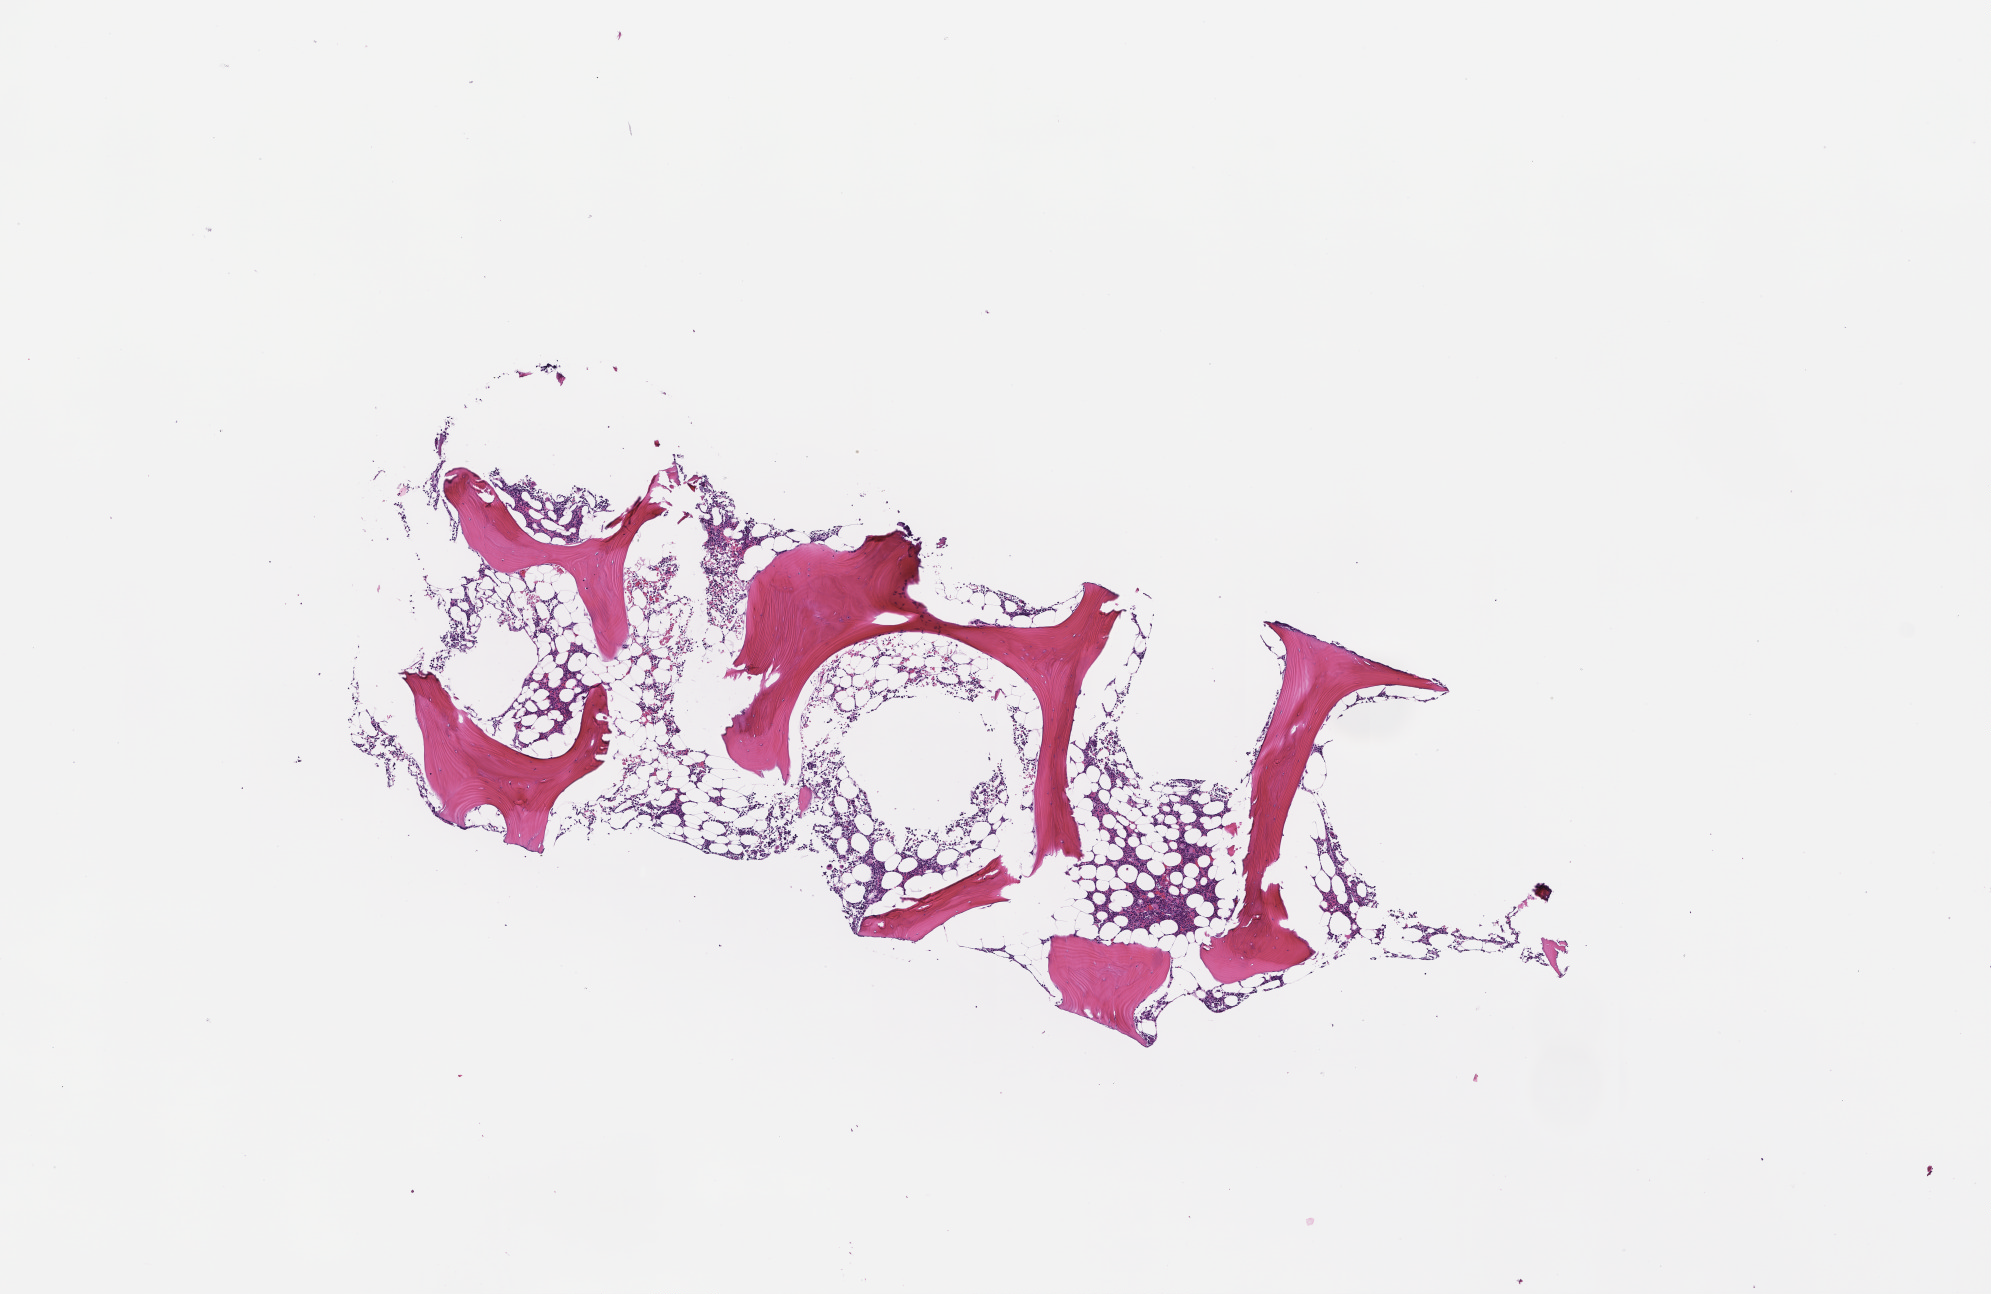
H&E whole-slide image, whole scanned area (about 8.0 x 5.2 mm) shown as a low-resolution overview; formalin-fixed paraffin-embedded section; tissue site: bone marrow. Patient: male.
This section: primary tumor. Diagnosis: Plasma Cell Myeloma.